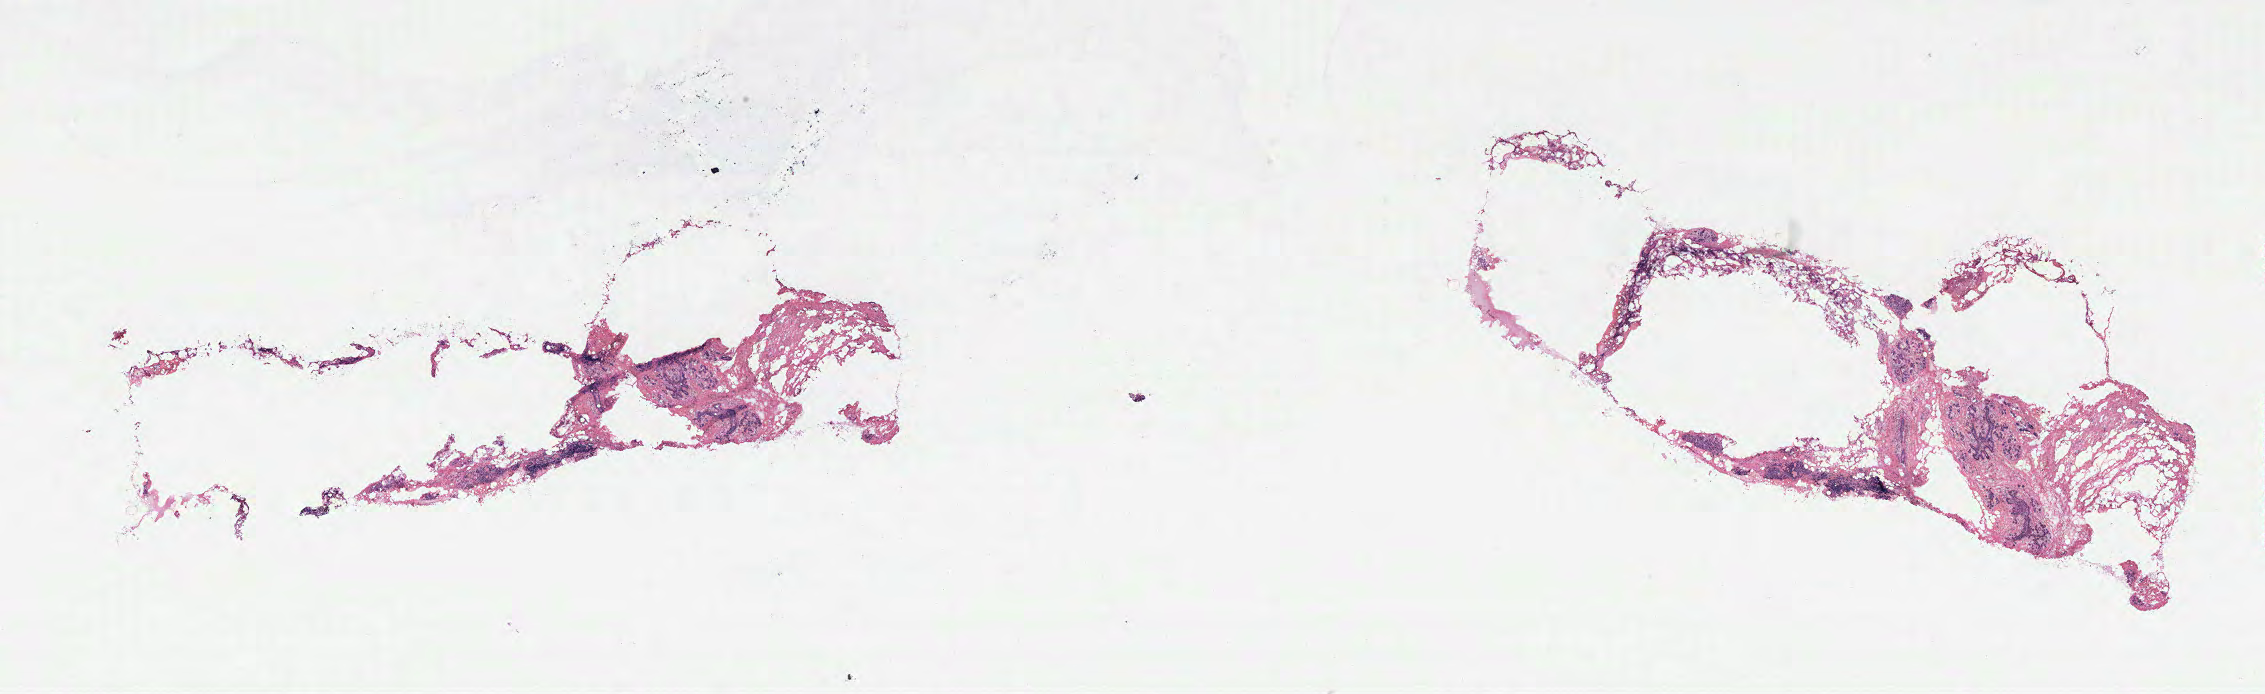
Digitized H&E tissue section (whole slide), a low-resolution overview of the entire scanned area, about 36.3 x 11.1 mm.
Specimen: breast, tissue type not recorded.